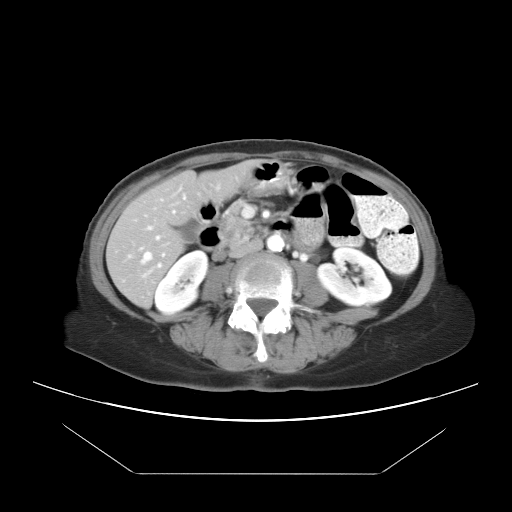
Contrast-enhanced abdominal CT, one axial slice. Slice 6 of 21 in the series (ordered by position). Reconstruction kernel STANDARD. 120 kVp. Intravenous contrast given. Soft-tissue window (W 400 / L 40 HU). 7.5 mm slice thickness. 512 × 512 image matrix, field of view 392 × 392 mm. Female patient, age 72 years. From the clinical record (not read from this slice): diagnosis: colorectal cancer liver metastases, imaged before liver resection; multiple liver metastases: yes; largest metastasis: 4 cm; disease in both lobes: yes.
Annotated regions visible in this slice (manually delineated by an expert):
- hepatic veins: bounding box <132,199,176,265> (left, top, right, bottom; pixels)
- liver: <108,167,246,307>
- planned liver remnant (the part of the liver to remain after resection): <108,167,246,294>
- portal vein (with intrahepatic branches): <140,226,165,257>